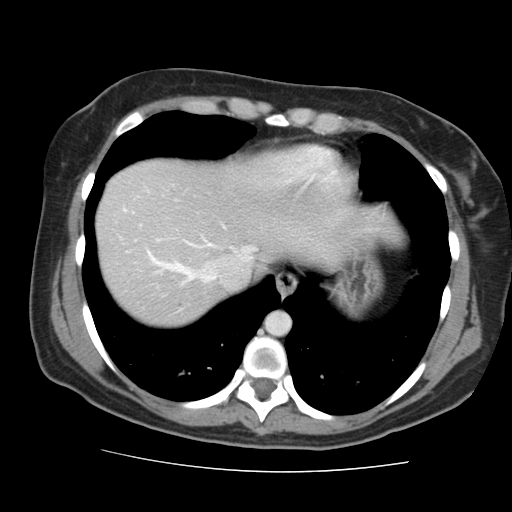
Contrast-enhanced abdominal CT, one axial slice; slice 130 of 144 in the series (ordered by position); intravenous contrast given; soft-tissue window (W 400 / L 40 HU); 512 × 512 image matrix, field of view 333 × 333 mm. Female patient, age 46 years. From the clinical record (not read from this slice): diagnosis: colorectal cancer liver metastases, imaged before liver resection; multiple liver metastases: no; largest metastasis: 2.8 cm.
Structures marked on this image (outlined manually by an expert reader):
- hepatic veins: bounding box (x1, y1, x2, y2) in pixels: (124, 210, 256, 283)
- liver: (97, 160, 339, 326)
- planned liver remnant (the part of the liver to remain after resection): (97, 160, 339, 326)
- portal vein (with intrahepatic branches): (148, 253, 180, 266)